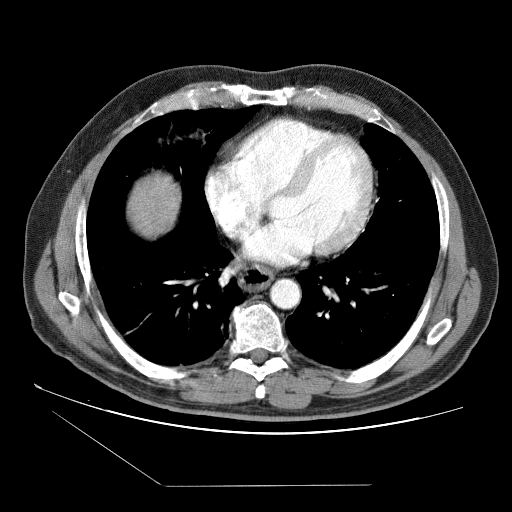
Contrast-enhanced abdominal CT (liver protocol), one axial slice. Slice 84 of 87 in the series (ordered by position). Soft-tissue window (W 400 / L 40 HU). 2.5 mm slice thickness. 512 × 512 image matrix, field of view 400 × 400 mm. From the clinical record (not read from this slice): diagnosis: hepatocellular carcinoma (patient treated with transarterial chemoembolisation; whether this scan precedes or follows treatment is not stated here); TNM stage (as recorded): Stage-II; Child-Pugh class: B.
Outlined on this slice (semi-automatic segmentation, software-assisted and operator-edited):
- liver parenchyma outside the tumour (the mass and vessels are separate outlines, so this box may not span the whole liver): box from (x=128, y=174) to (x=180, y=234) px